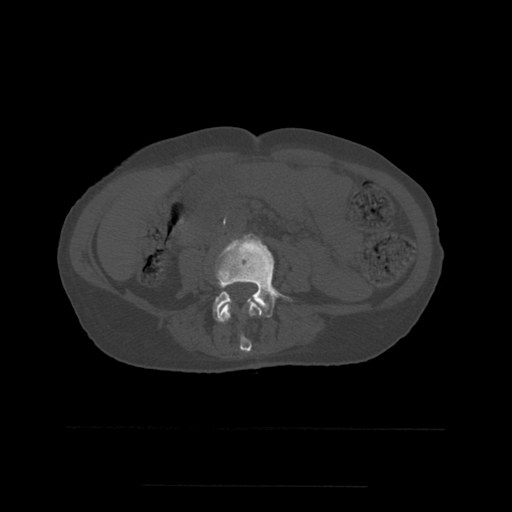
CT including the spine, one axial slice; position 175 of 544 along the scan axis; bone window (W 1800 / L 400 HU); 1.25 mm slice thickness; 512 × 512 image matrix, field of view 350 × 350 mm. Patient age 58 years. Case-level facts recorded for this patient, not image findings: primary cancer: lung.
Outlined on this slice (semi-automatically segmented with operator editing):
- L3 vertebra: bounding box [x1, y1, x2, y2] px = [218, 299, 262, 353]
- L4 vertebra: [213, 234, 293, 322]